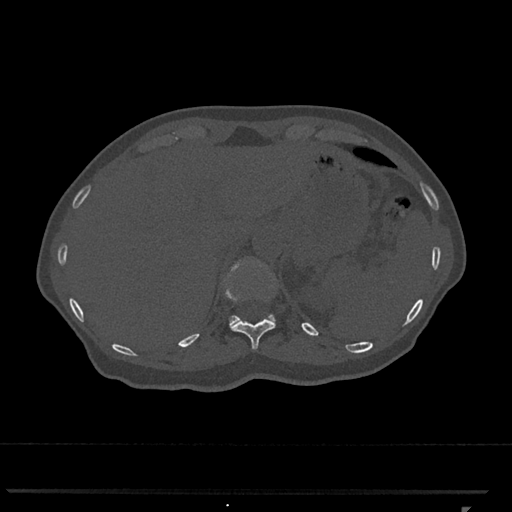
CT including the spine, one axial slice; position 501 of 793 along the scan axis; bone window (W 1800 / L 400 HU); 512 × 512 image matrix, field of view 380 × 380 mm. Female patient, age 62 years. From the clinical record (not read from this slice): primary cancer: renal.
Annotated regions visible in this slice (semi-automatically segmented with operator editing):
- T11 vertebra: bounding box <230,261,276,350> (left, top, right, bottom; pixels)
- T12 vertebra: <224,260,275,325>